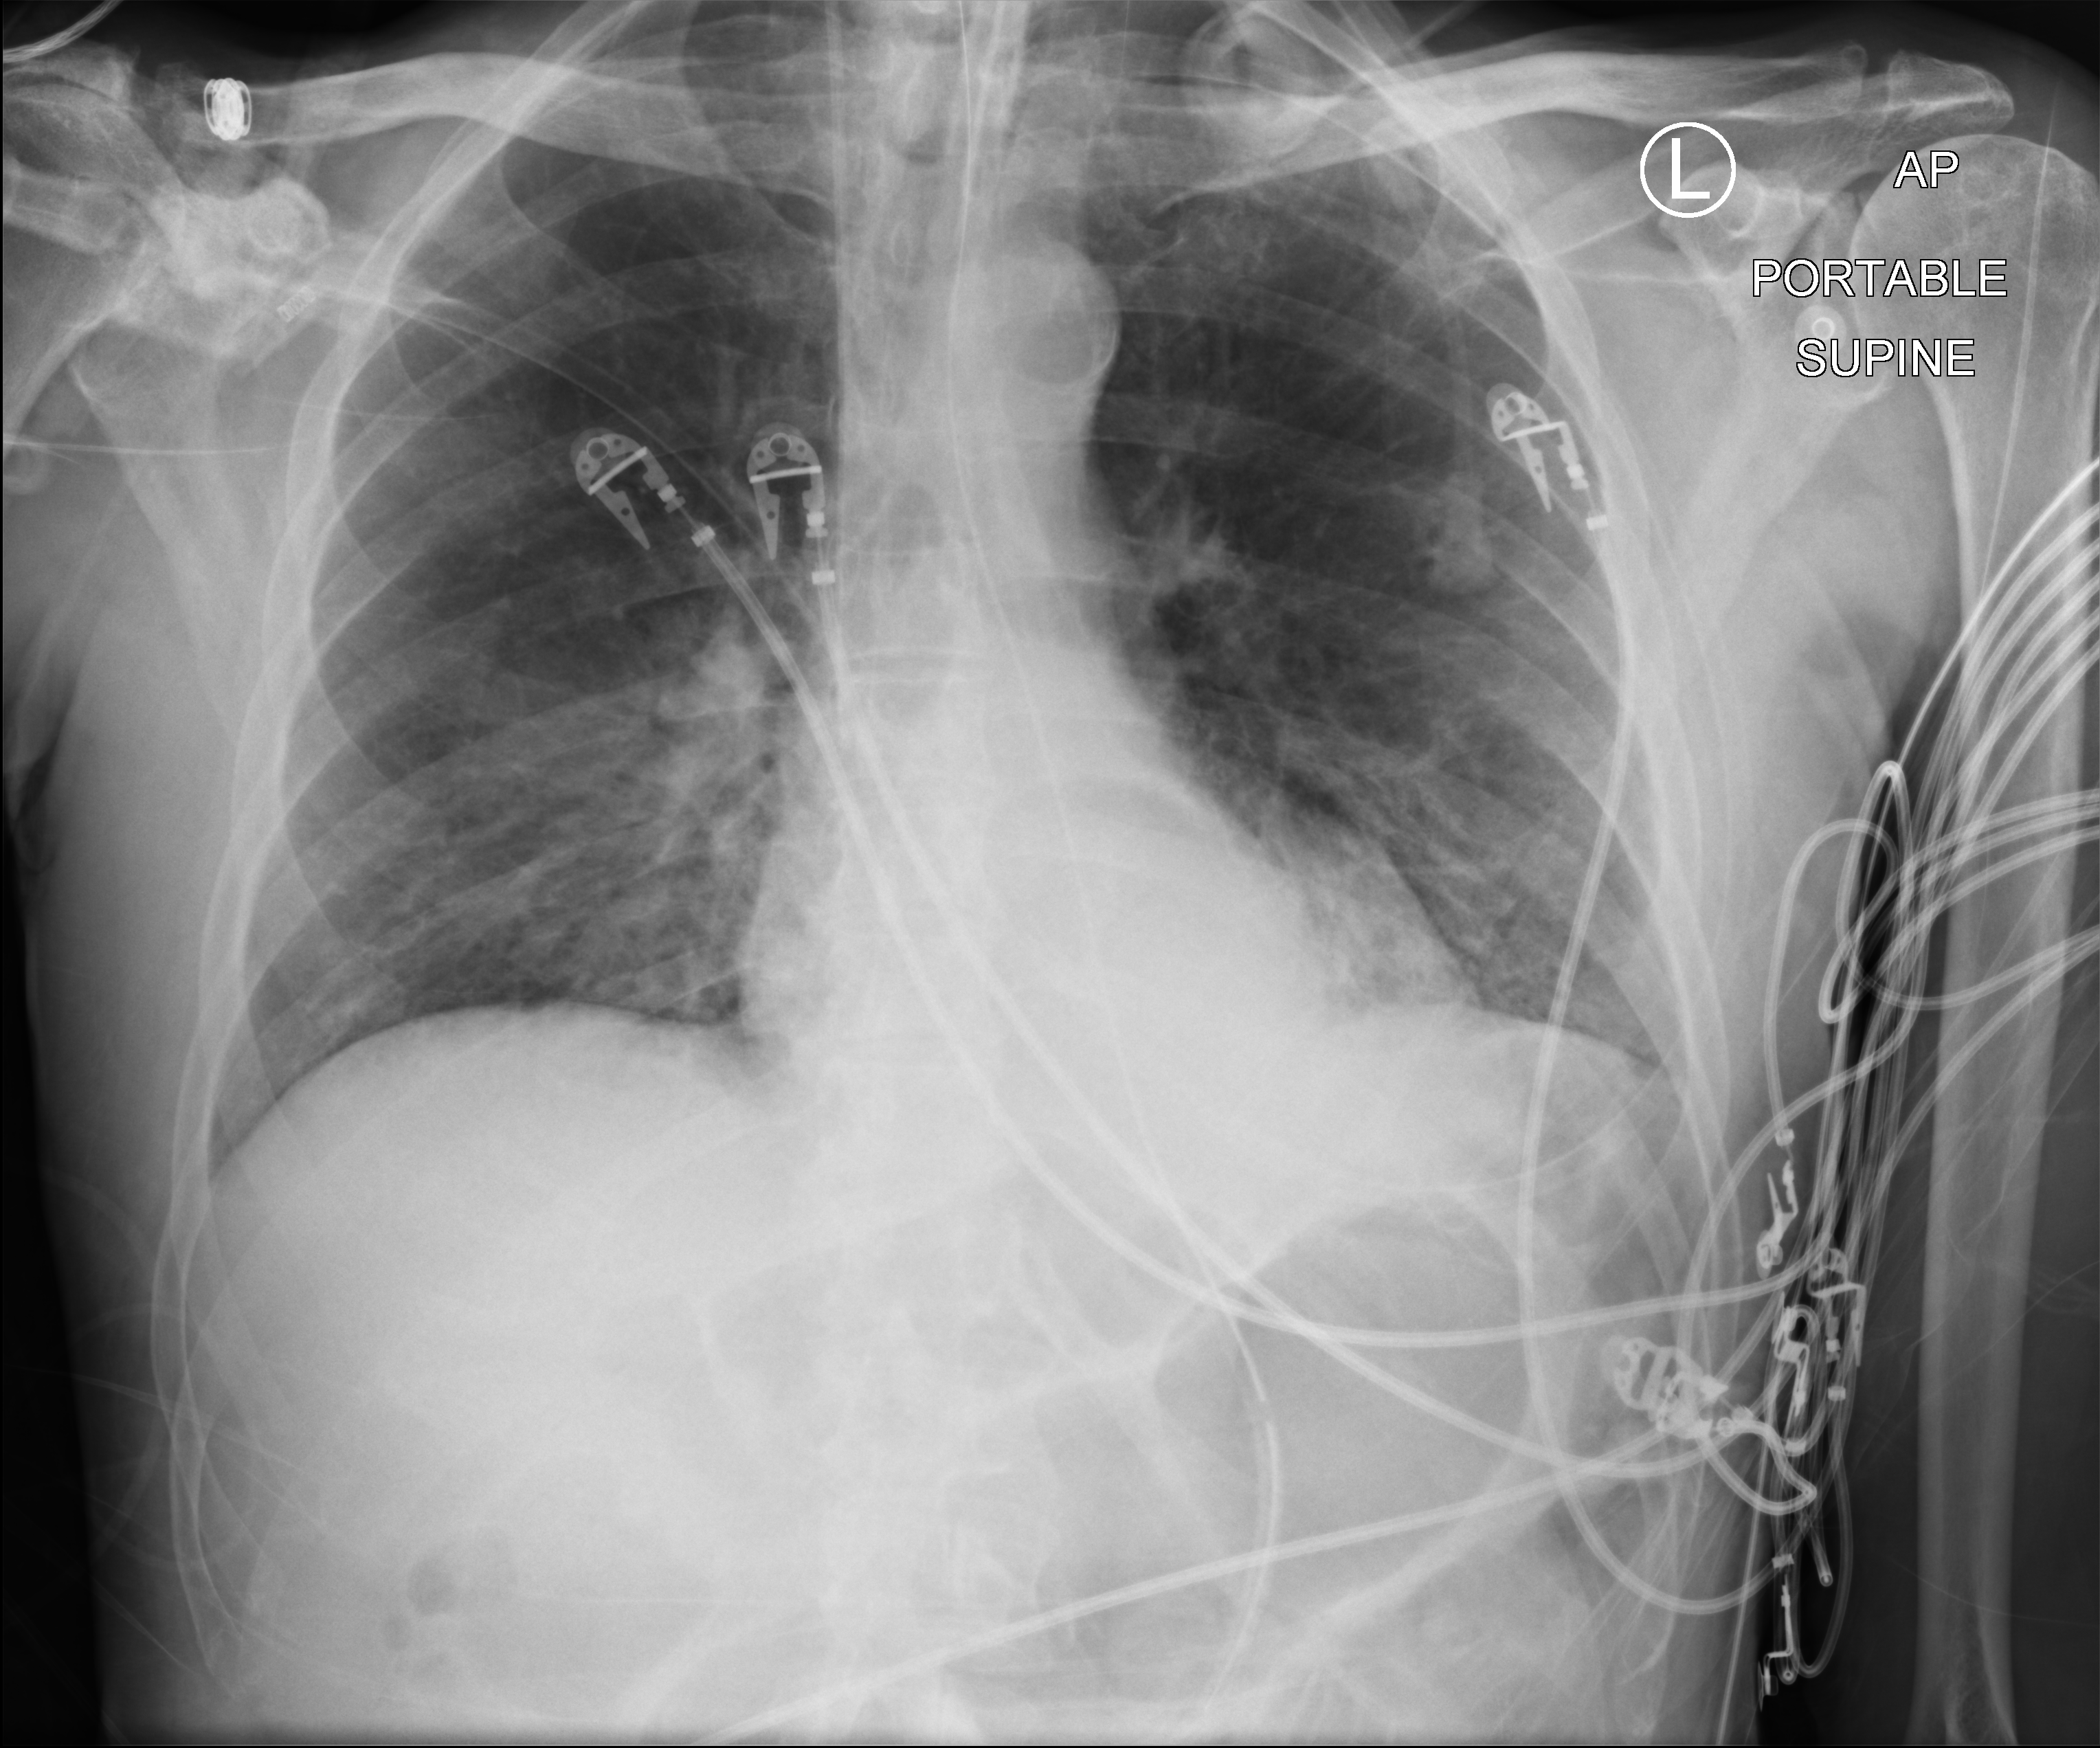
Bedside chest radiograph (computed radiography); anteroposterior (AP) projection. Patient hospitalised with COVID-19; male, aged 75–90 years.
Admission-level facts for this patient (not findings on this image; timing relative to this image not recorded): admitted to intensive care during this hospital stay: yes.